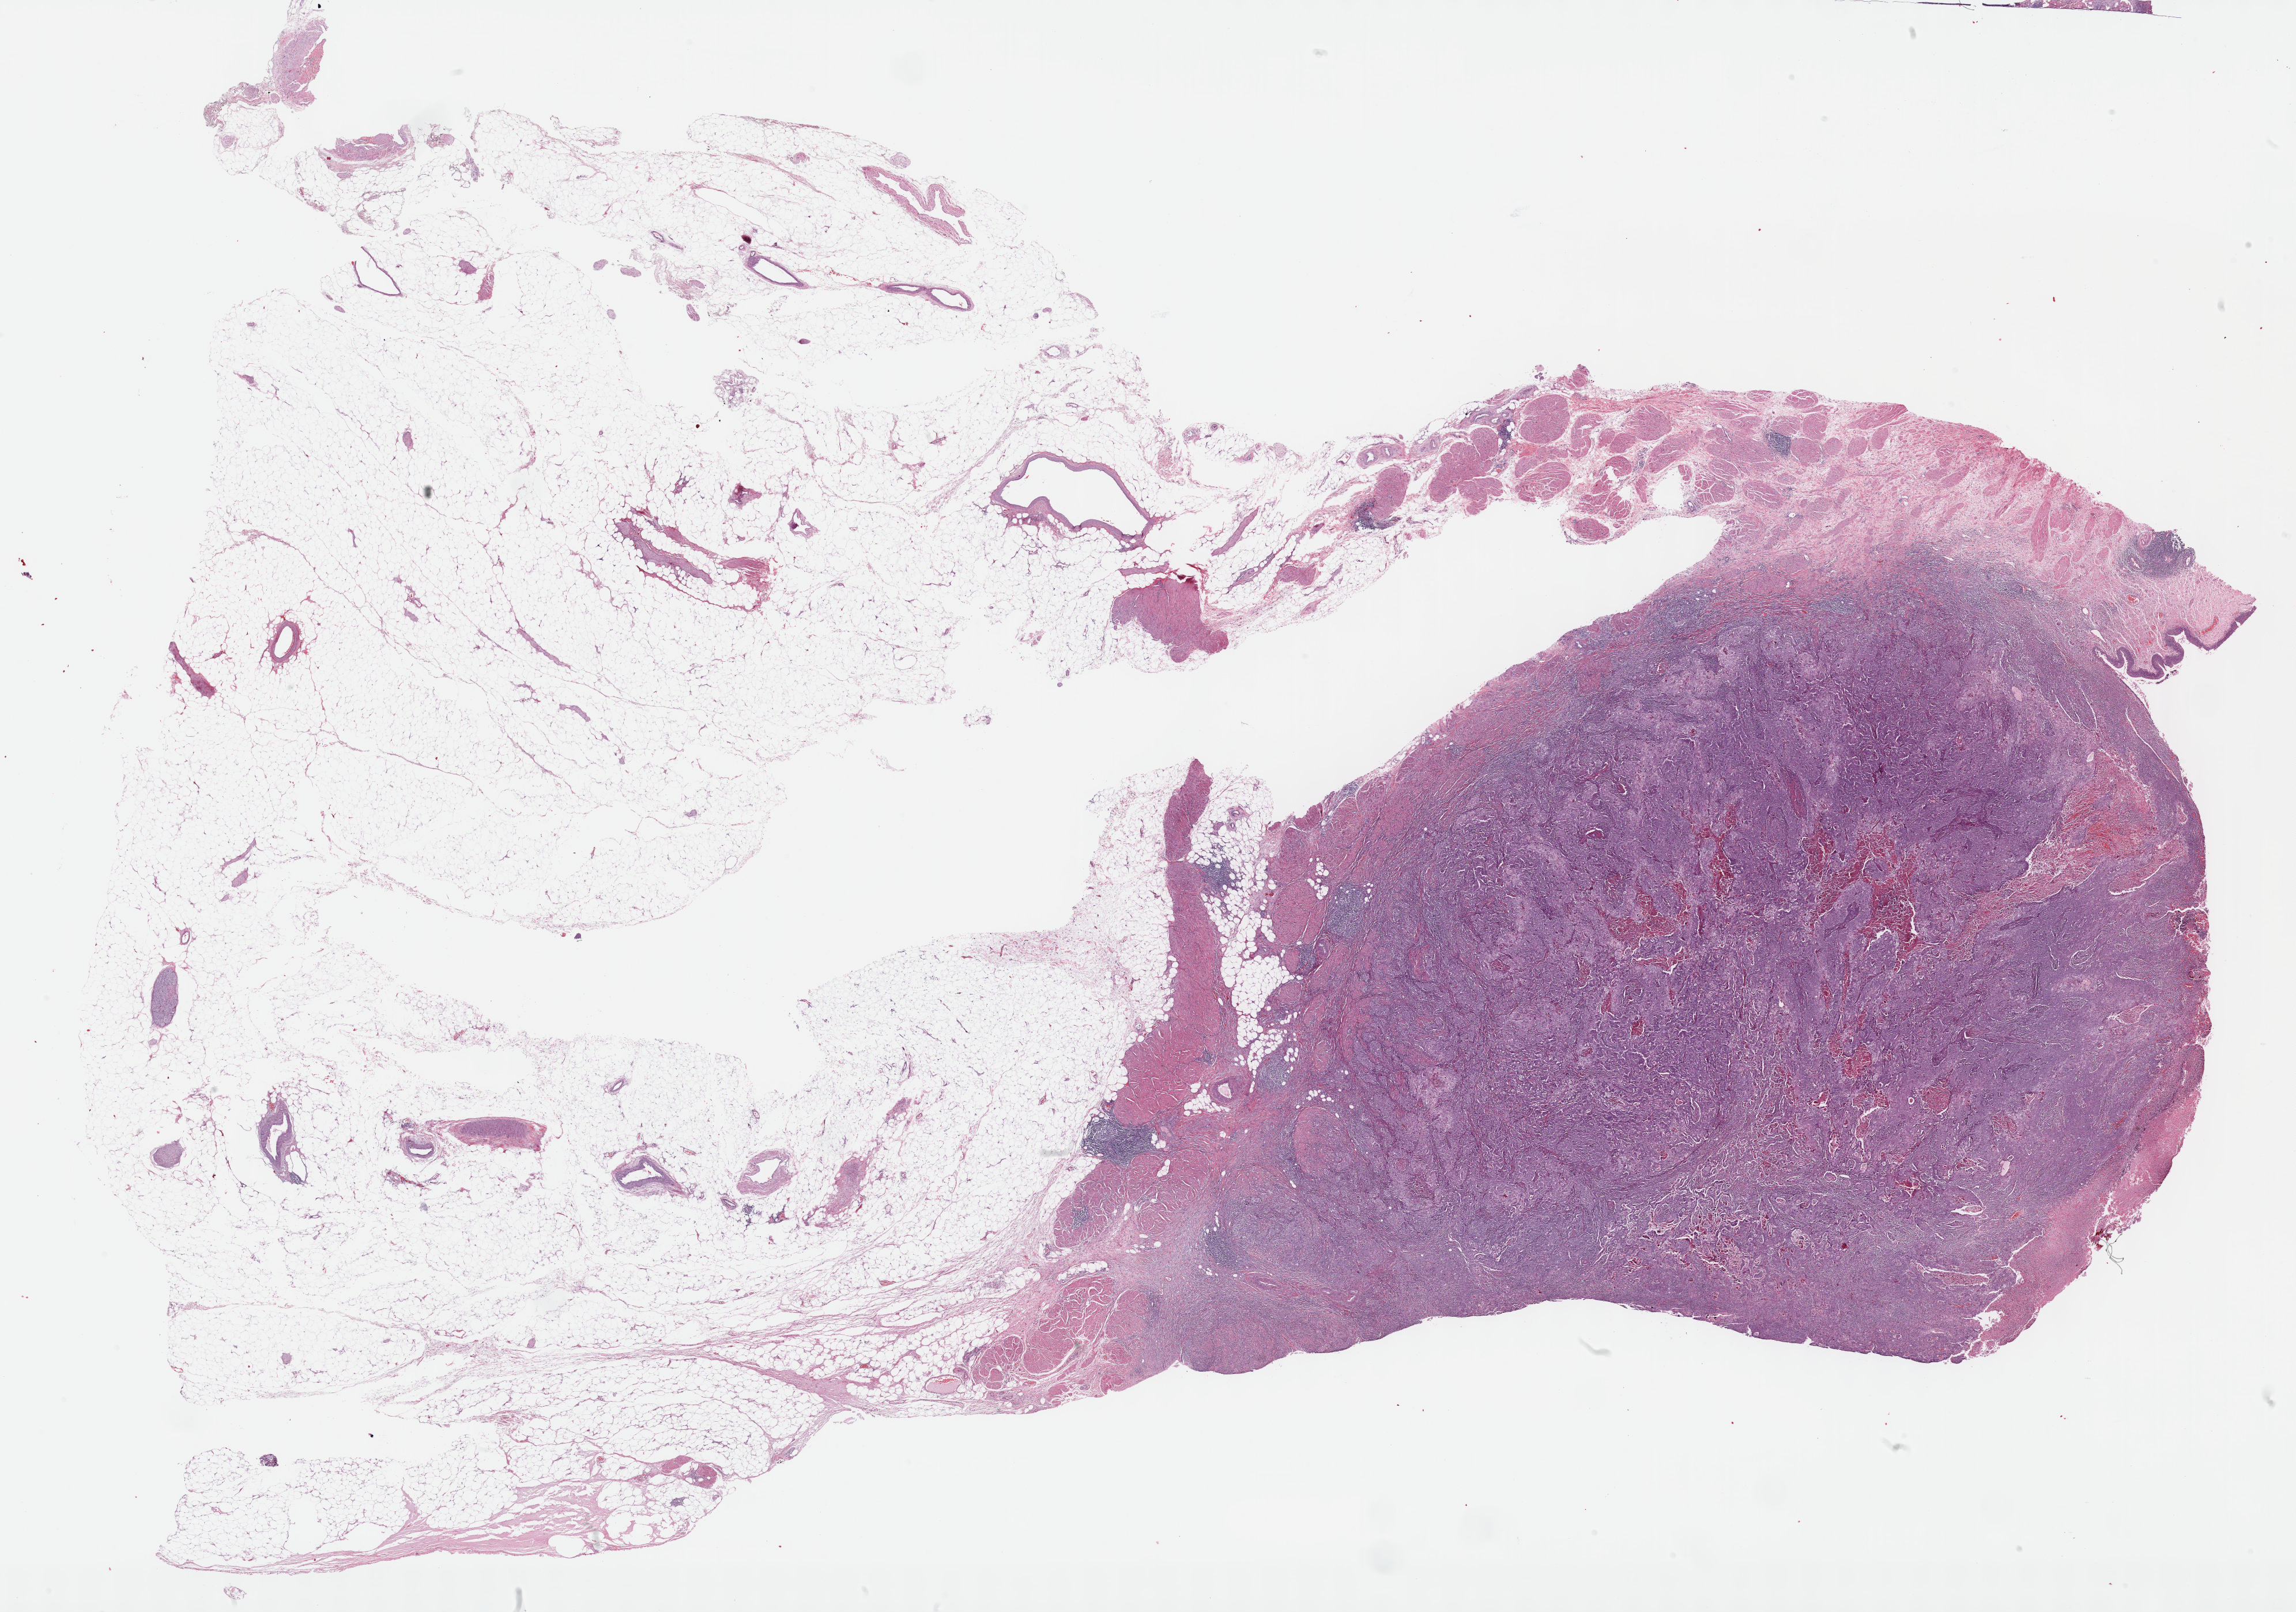
H&E whole-slide image — a low-resolution overview of the entire scanned area, about 32.2 x 22.6 mm (acquisition: 40x scan), FFPE section, sample: primary tumour, bladder. Patient: male, age at initial diagnosis 73 years.
Histologic diagnosis: Transitional cell carcinoma.